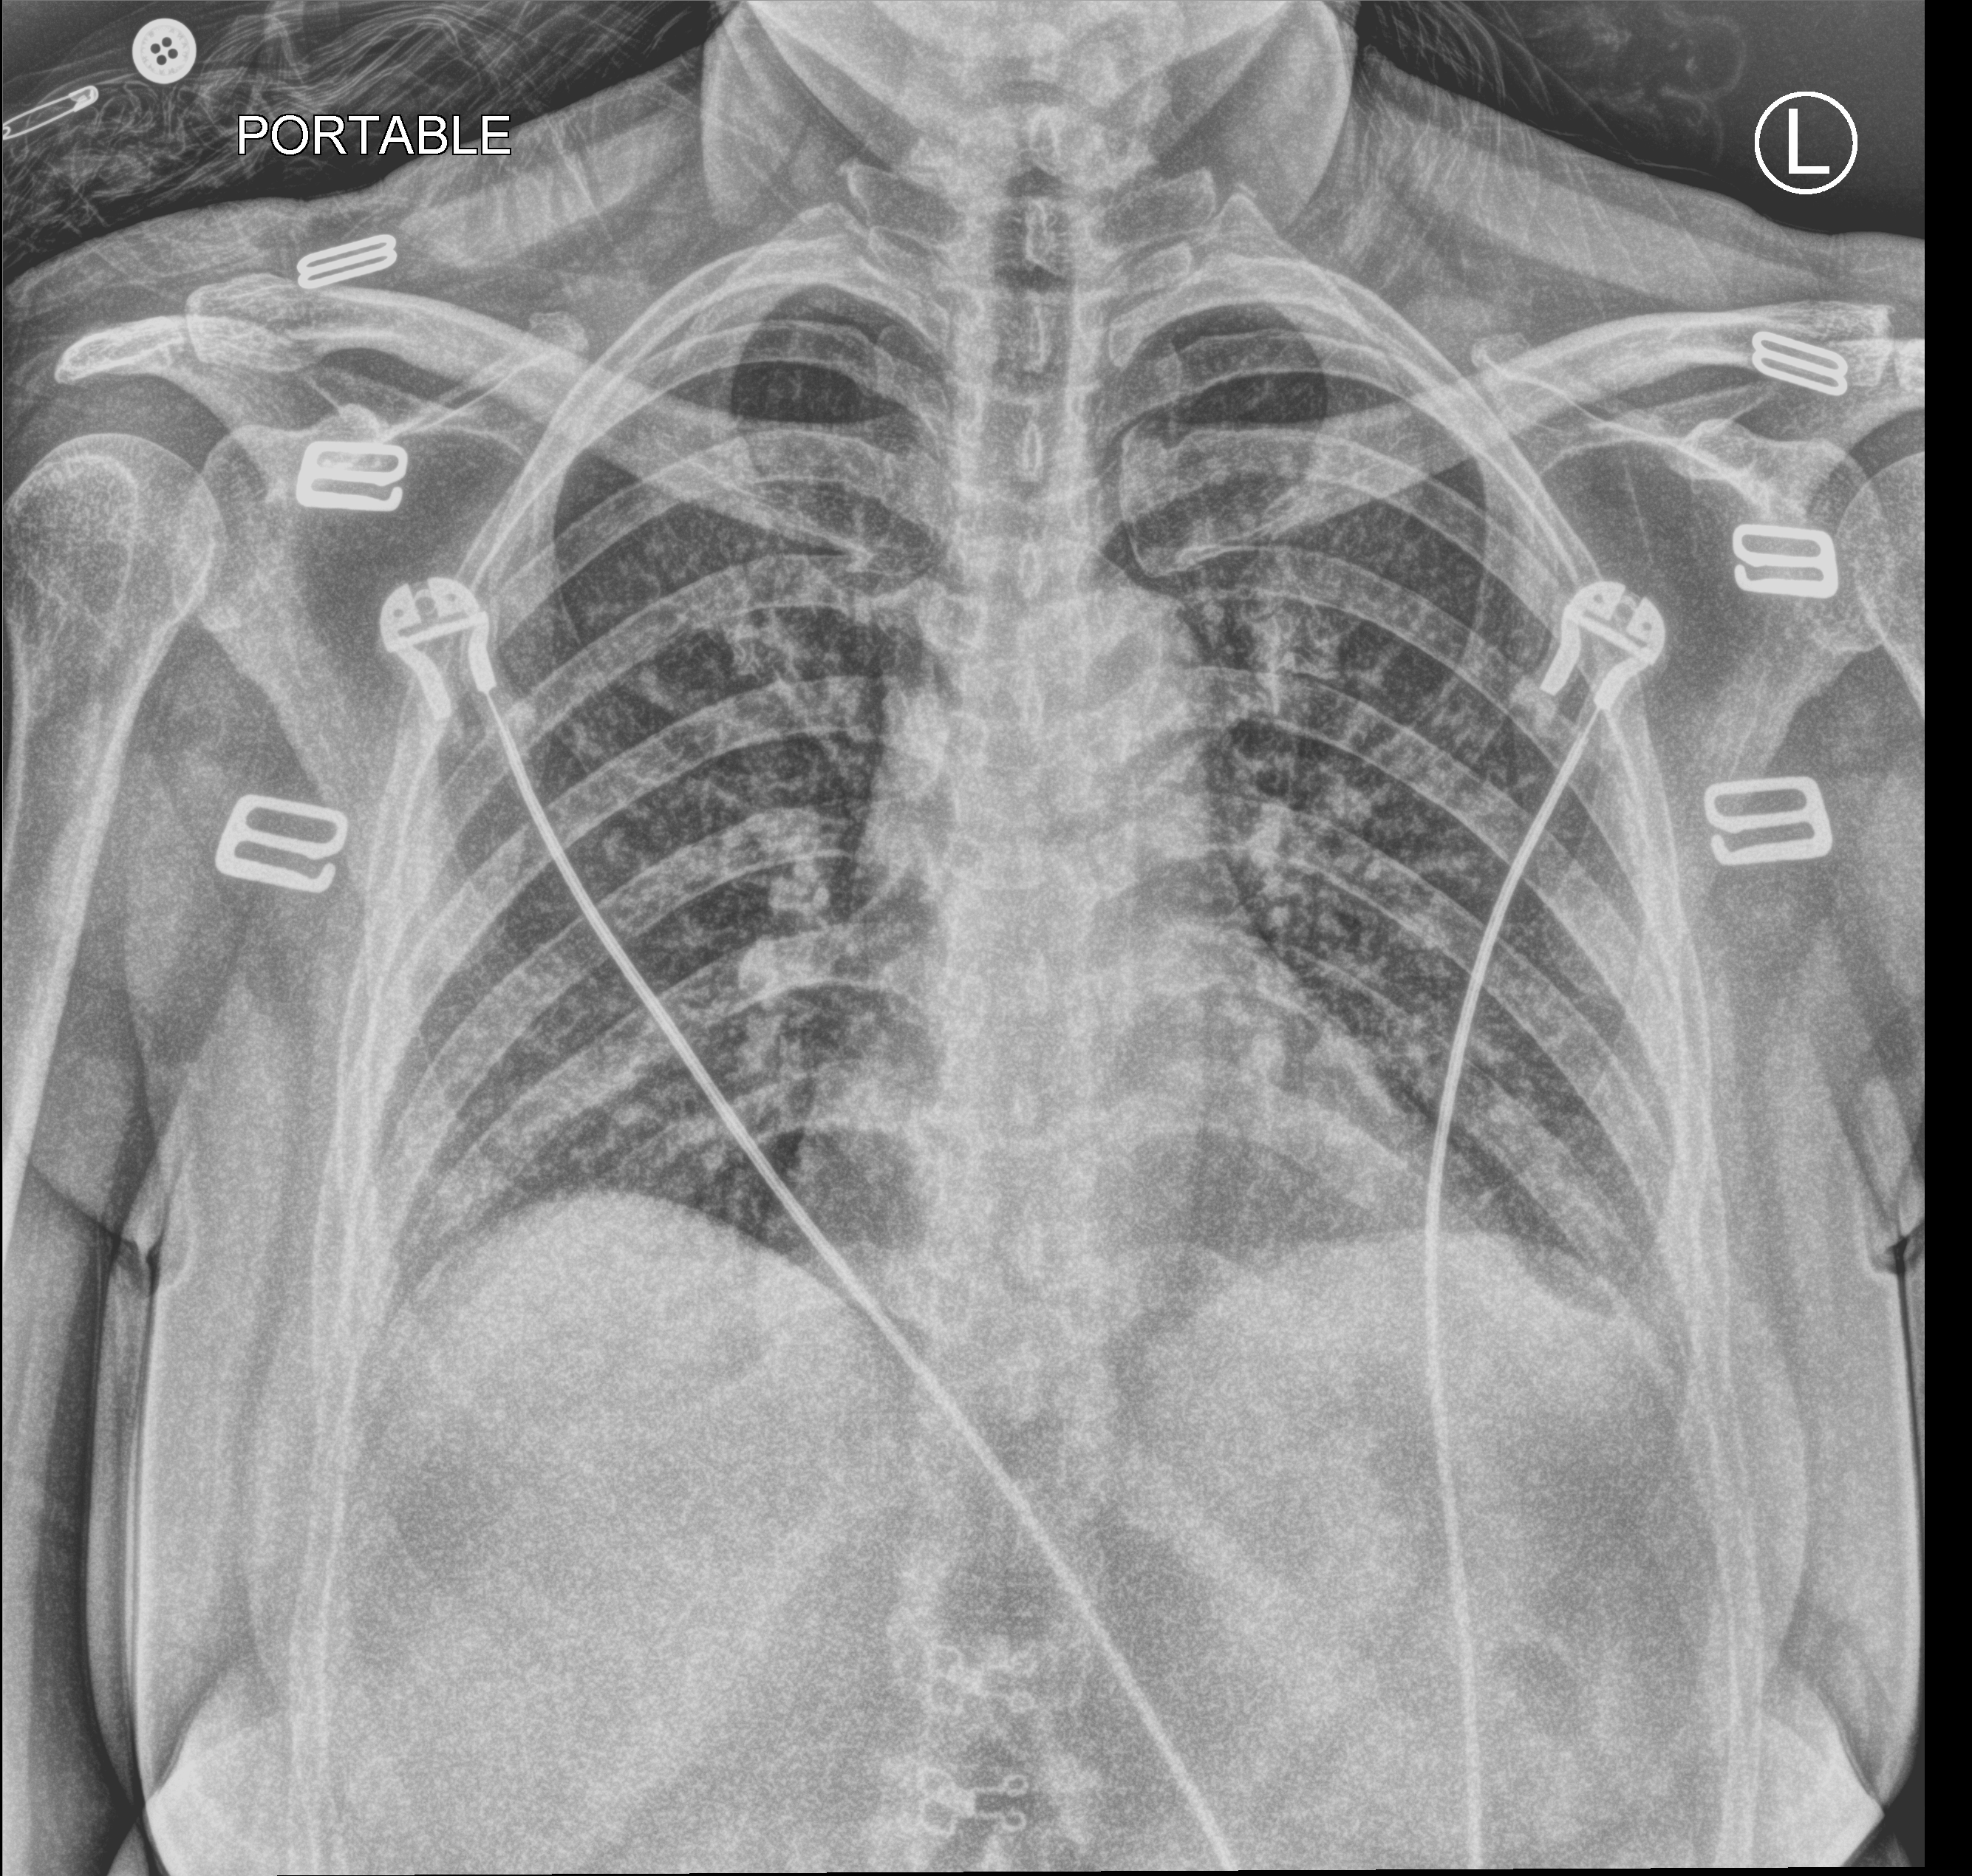
Portable chest radiograph; anteroposterior (AP) projection. Female patient hospitalised with COVID-19, age 18–59 years.
Hospital-stay facts (about this admission, not read from this image; timing relative to this image not recorded):
- other chronic lung disease (admission record): no
- mechanically ventilated during this hospital stay: no
- admitted to intensive care during this hospital stay: no